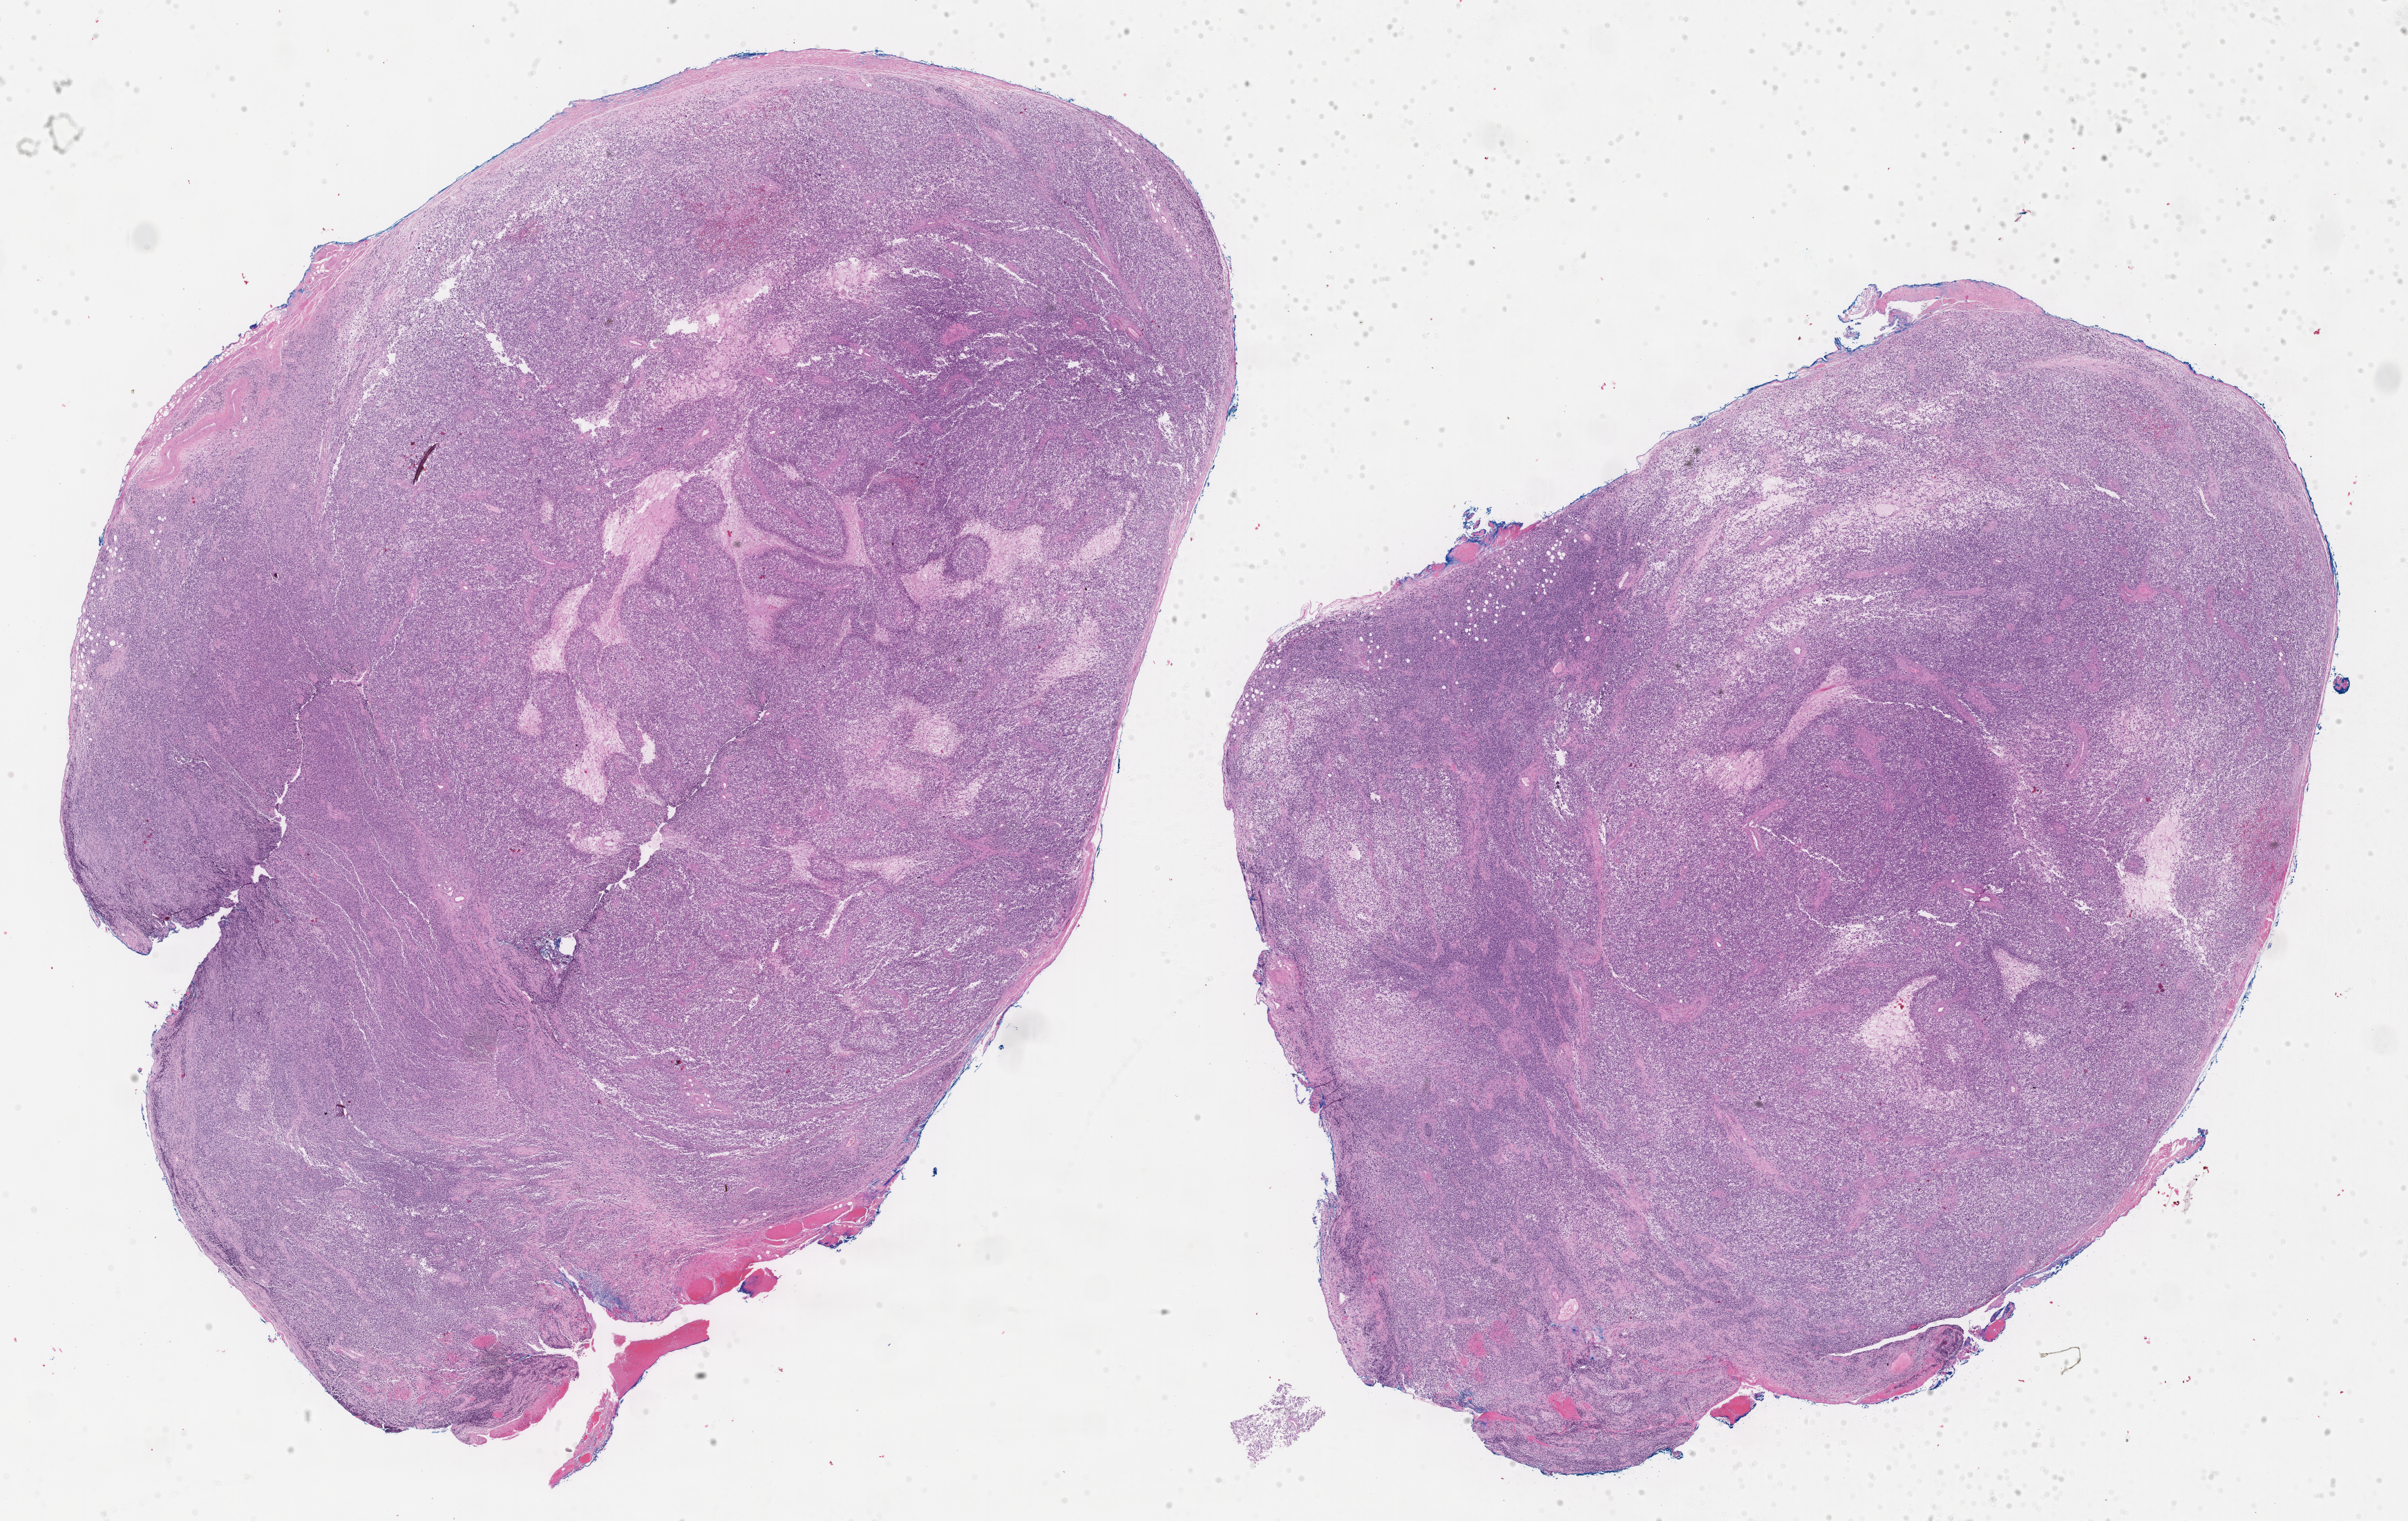
Whole-slide image, haematoxylin and eosin stain of tumor tissue, shown as a low-resolution overview of the whole scanned area (about 28.2 x 17.8 mm). Formalin-fixed paraffin-embedded section. Sample anatomic site: eye, orbit-left. Female patient, age at diagnosis 2.3 years.
Diagnosis: rhabdomyosarcoma; histological classification: embryonal rhabdomyosarcoma.